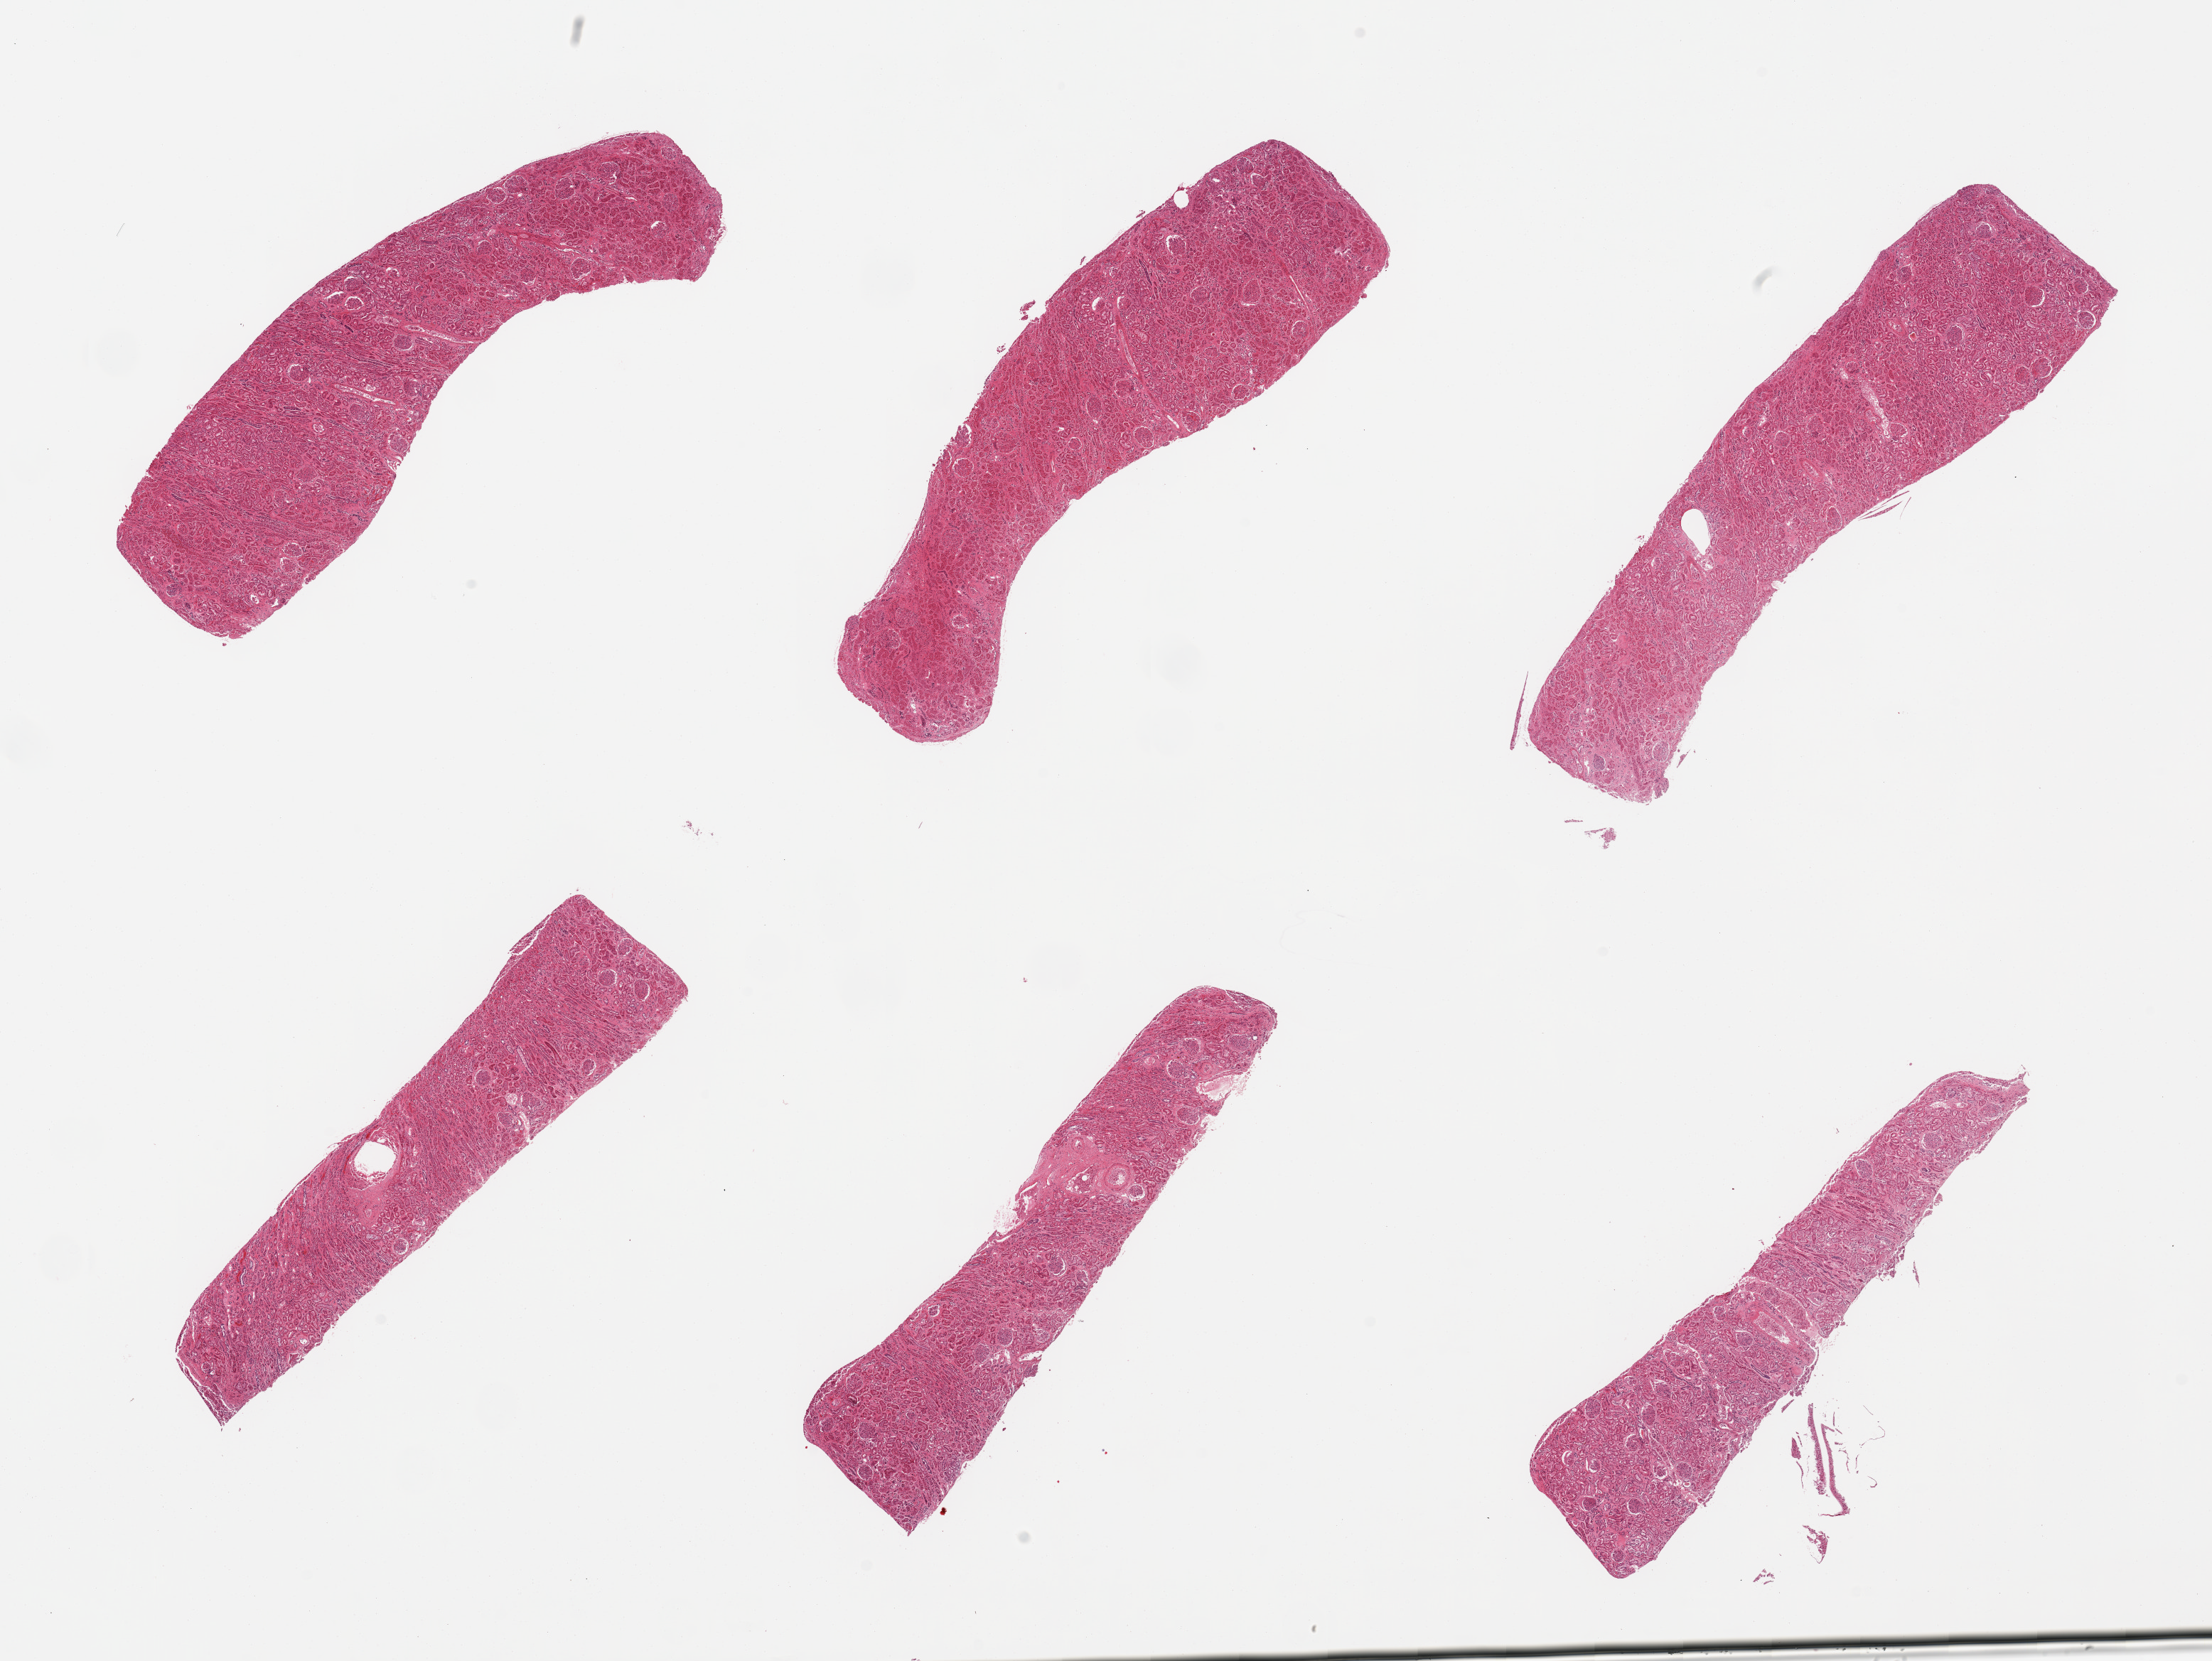
Haematoxylin and eosin whole-slide image — shown as a low-resolution overview of the whole scanned area (about 24.6 x 18.5 mm, acquisition: 20x scan); PAXgene-fixed, paraffin-embedded tissue; section of renal cortex (target tissue); tissue donor sample. Donor sex: female.
Pathologist's review note for this sample: 6 pieces; glomeruli in all sections, some interstitial fibrosis.